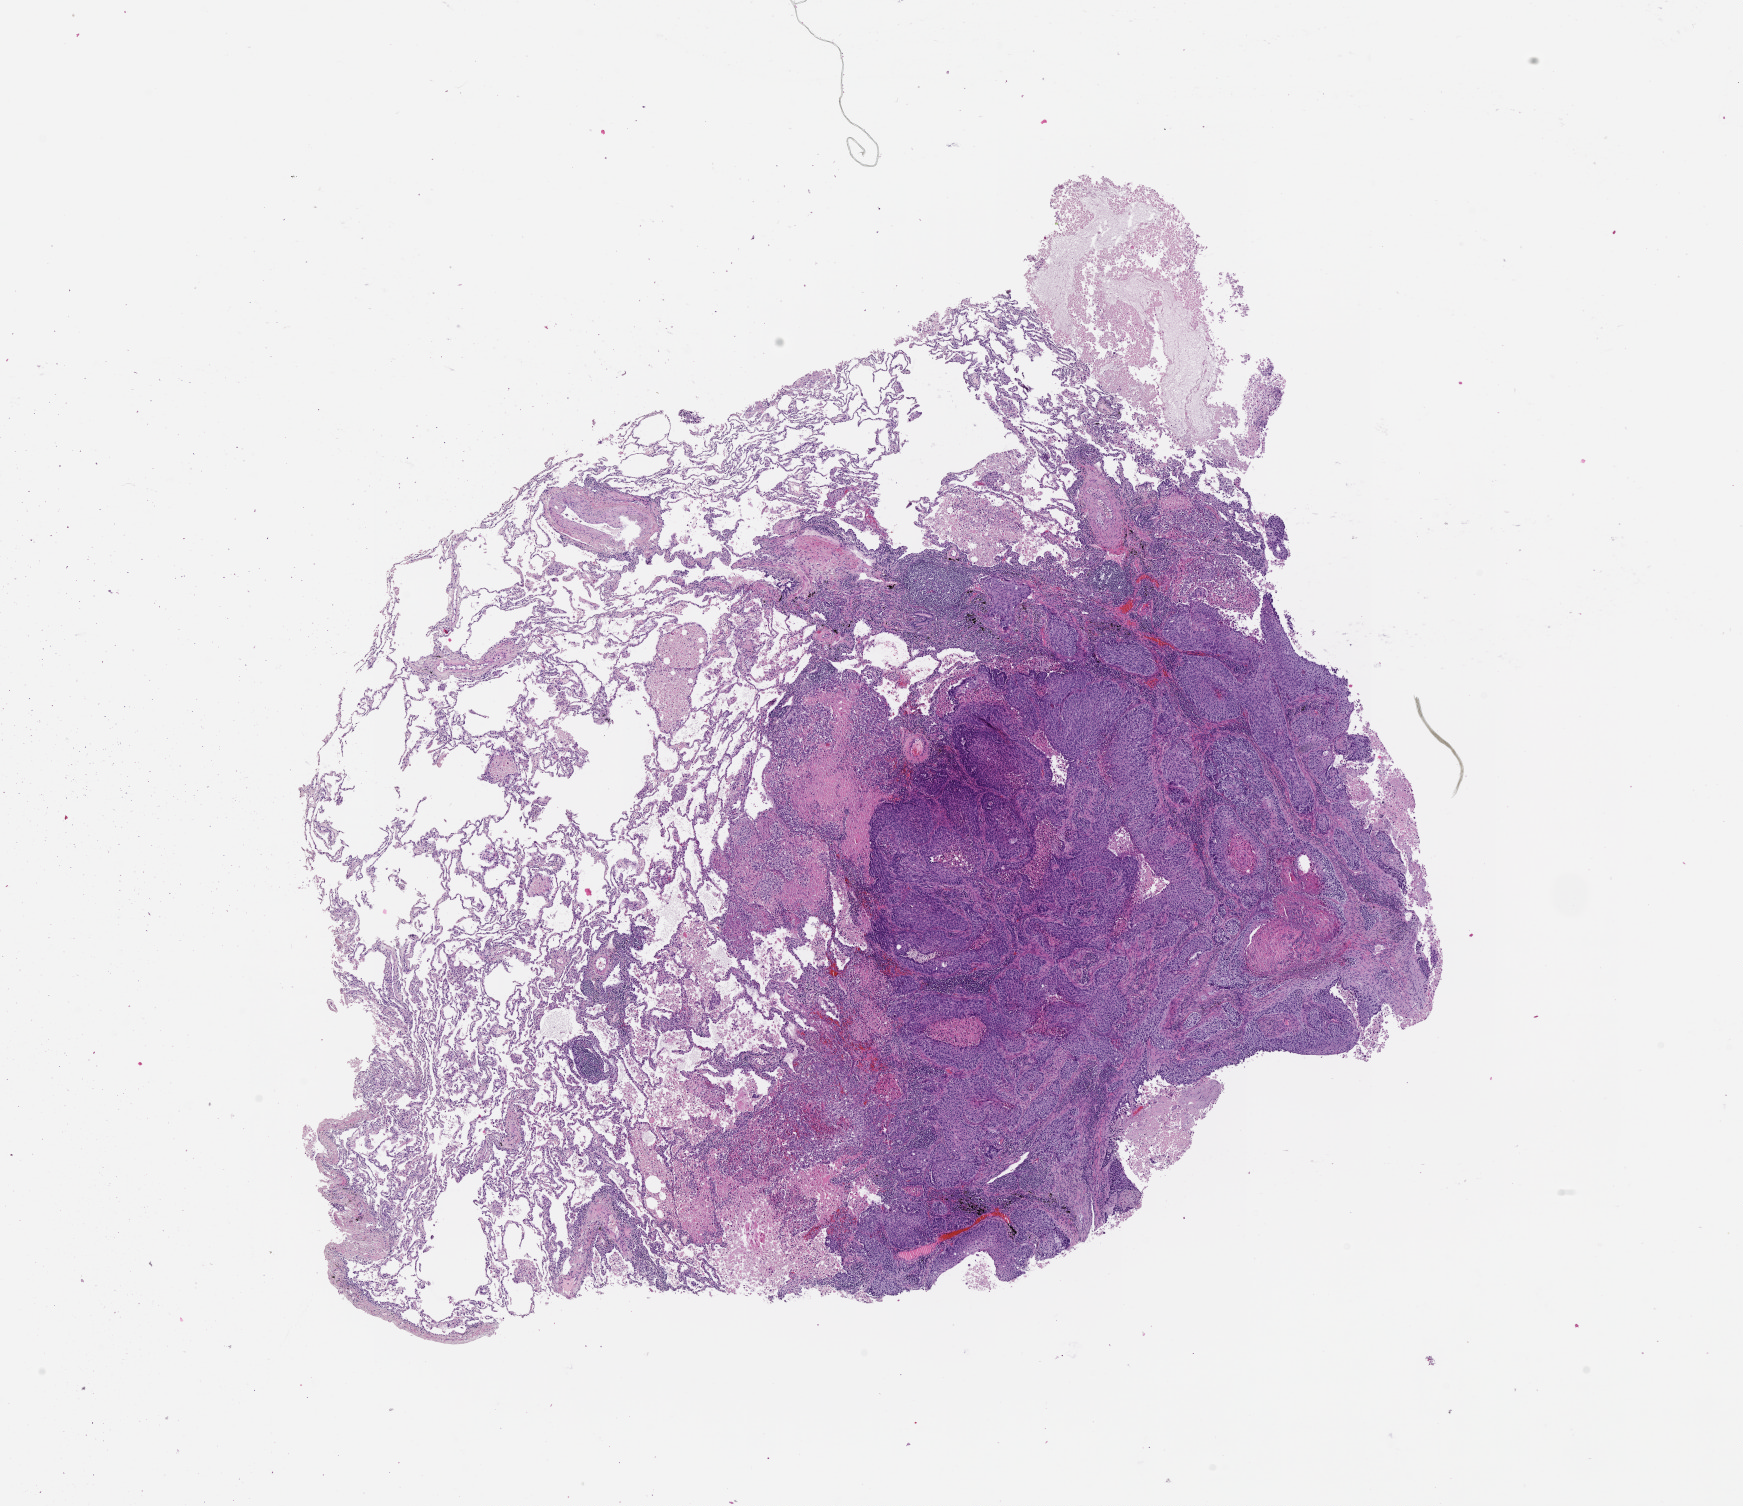
Whole-slide histology image, H&E-stained — low-resolution overview of the scanned area, about 14.0 x 12.1 mm; lung, tumour tissue. 67-year-old male patient.
Patient diagnosis (cohort enrolment): squamous cell carcinoma (lung).